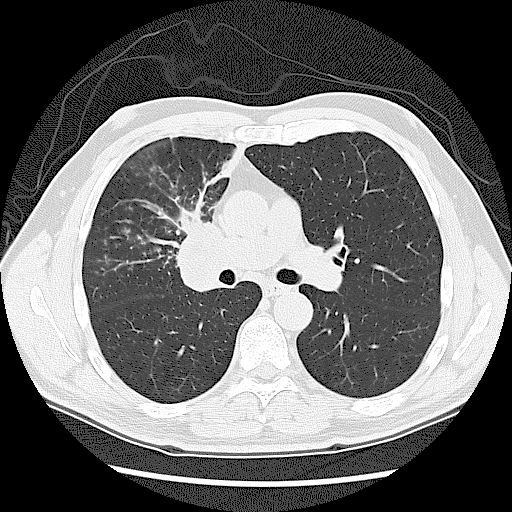
Axial slice from a low-dose chest CT screening exam. First (baseline) screen. Lung window (W 1500 / L -600 HU). 2.5 mm slice thickness. 120 kVp. Slice 57 of 131 in the series. 512 × 512 image matrix, field of view 360 × 360 mm. Male participant, aged 60 years at enrolment. Current smoker at enrolment.
• Expert reader's lesion annotation, bounding box <158,217,241,309> (left, top, right, bottom; pixels).
• No non-calcified nodule or mass ≥4 mm was recorded by the screening reader at this exam.
• Lung cancer was diagnosed 41 days after this screen: small cell carcinoma, NOS, right upper lobe, stage IIIA (AJCC 6th edition).